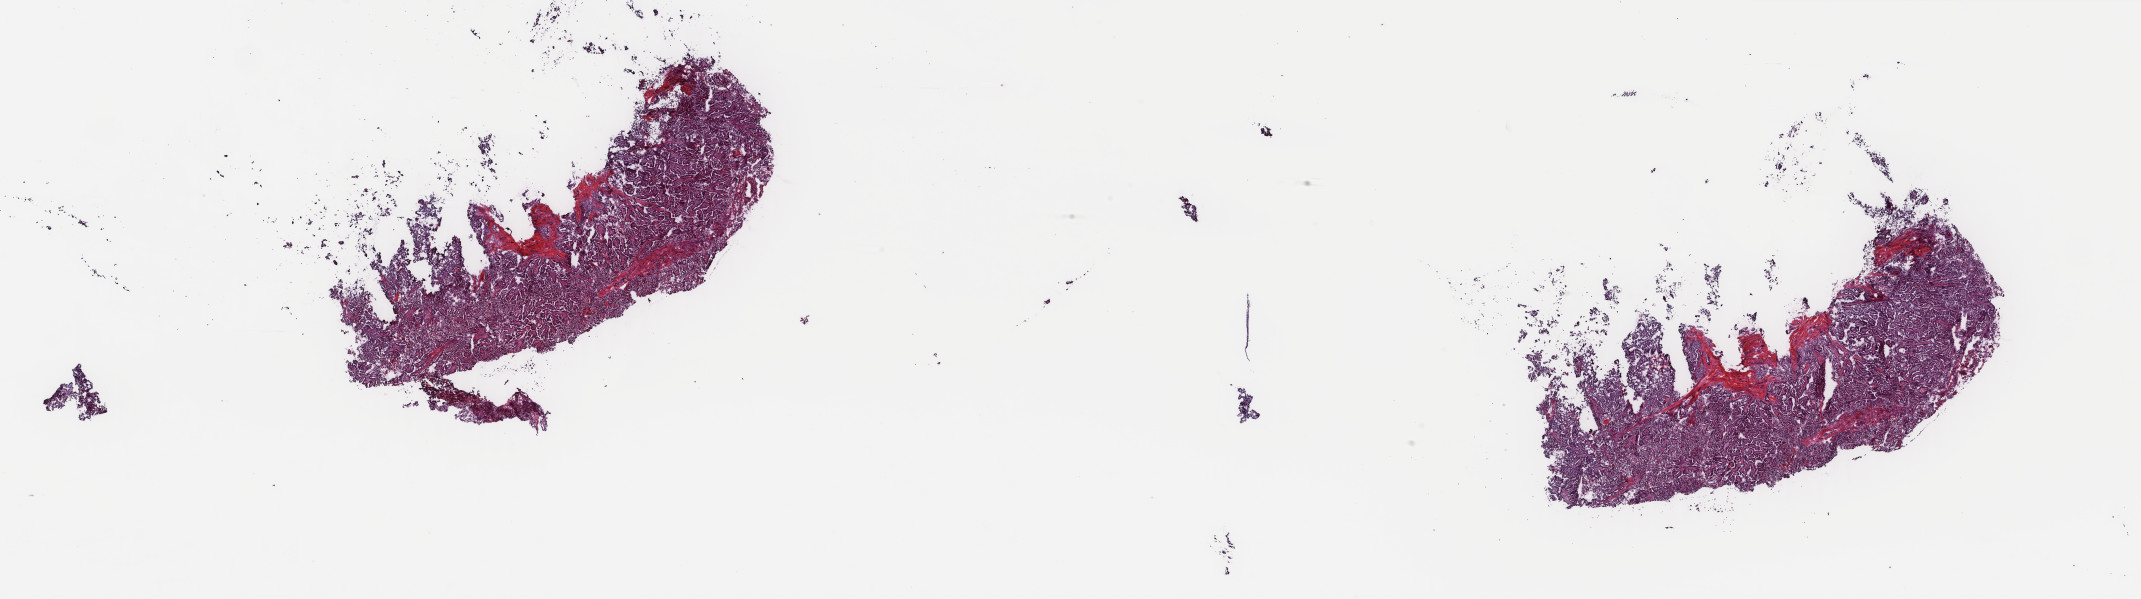
Digitized Hematoxylin and eosin (H&E) stained tissue section (whole slide), low-resolution overview of the scanned area, about 34.0 x 9.5 mm, frozen section from the top of the tissue portion, primary tumour sample from the thyroid. Male patient; age at initial diagnosis 51 years. Composition of this section per pathologist review: tumour cells 100%, tumour nuclei 90%.
Diagnosis: Papillary adenocarcinoma, NOS (thyroid gland).